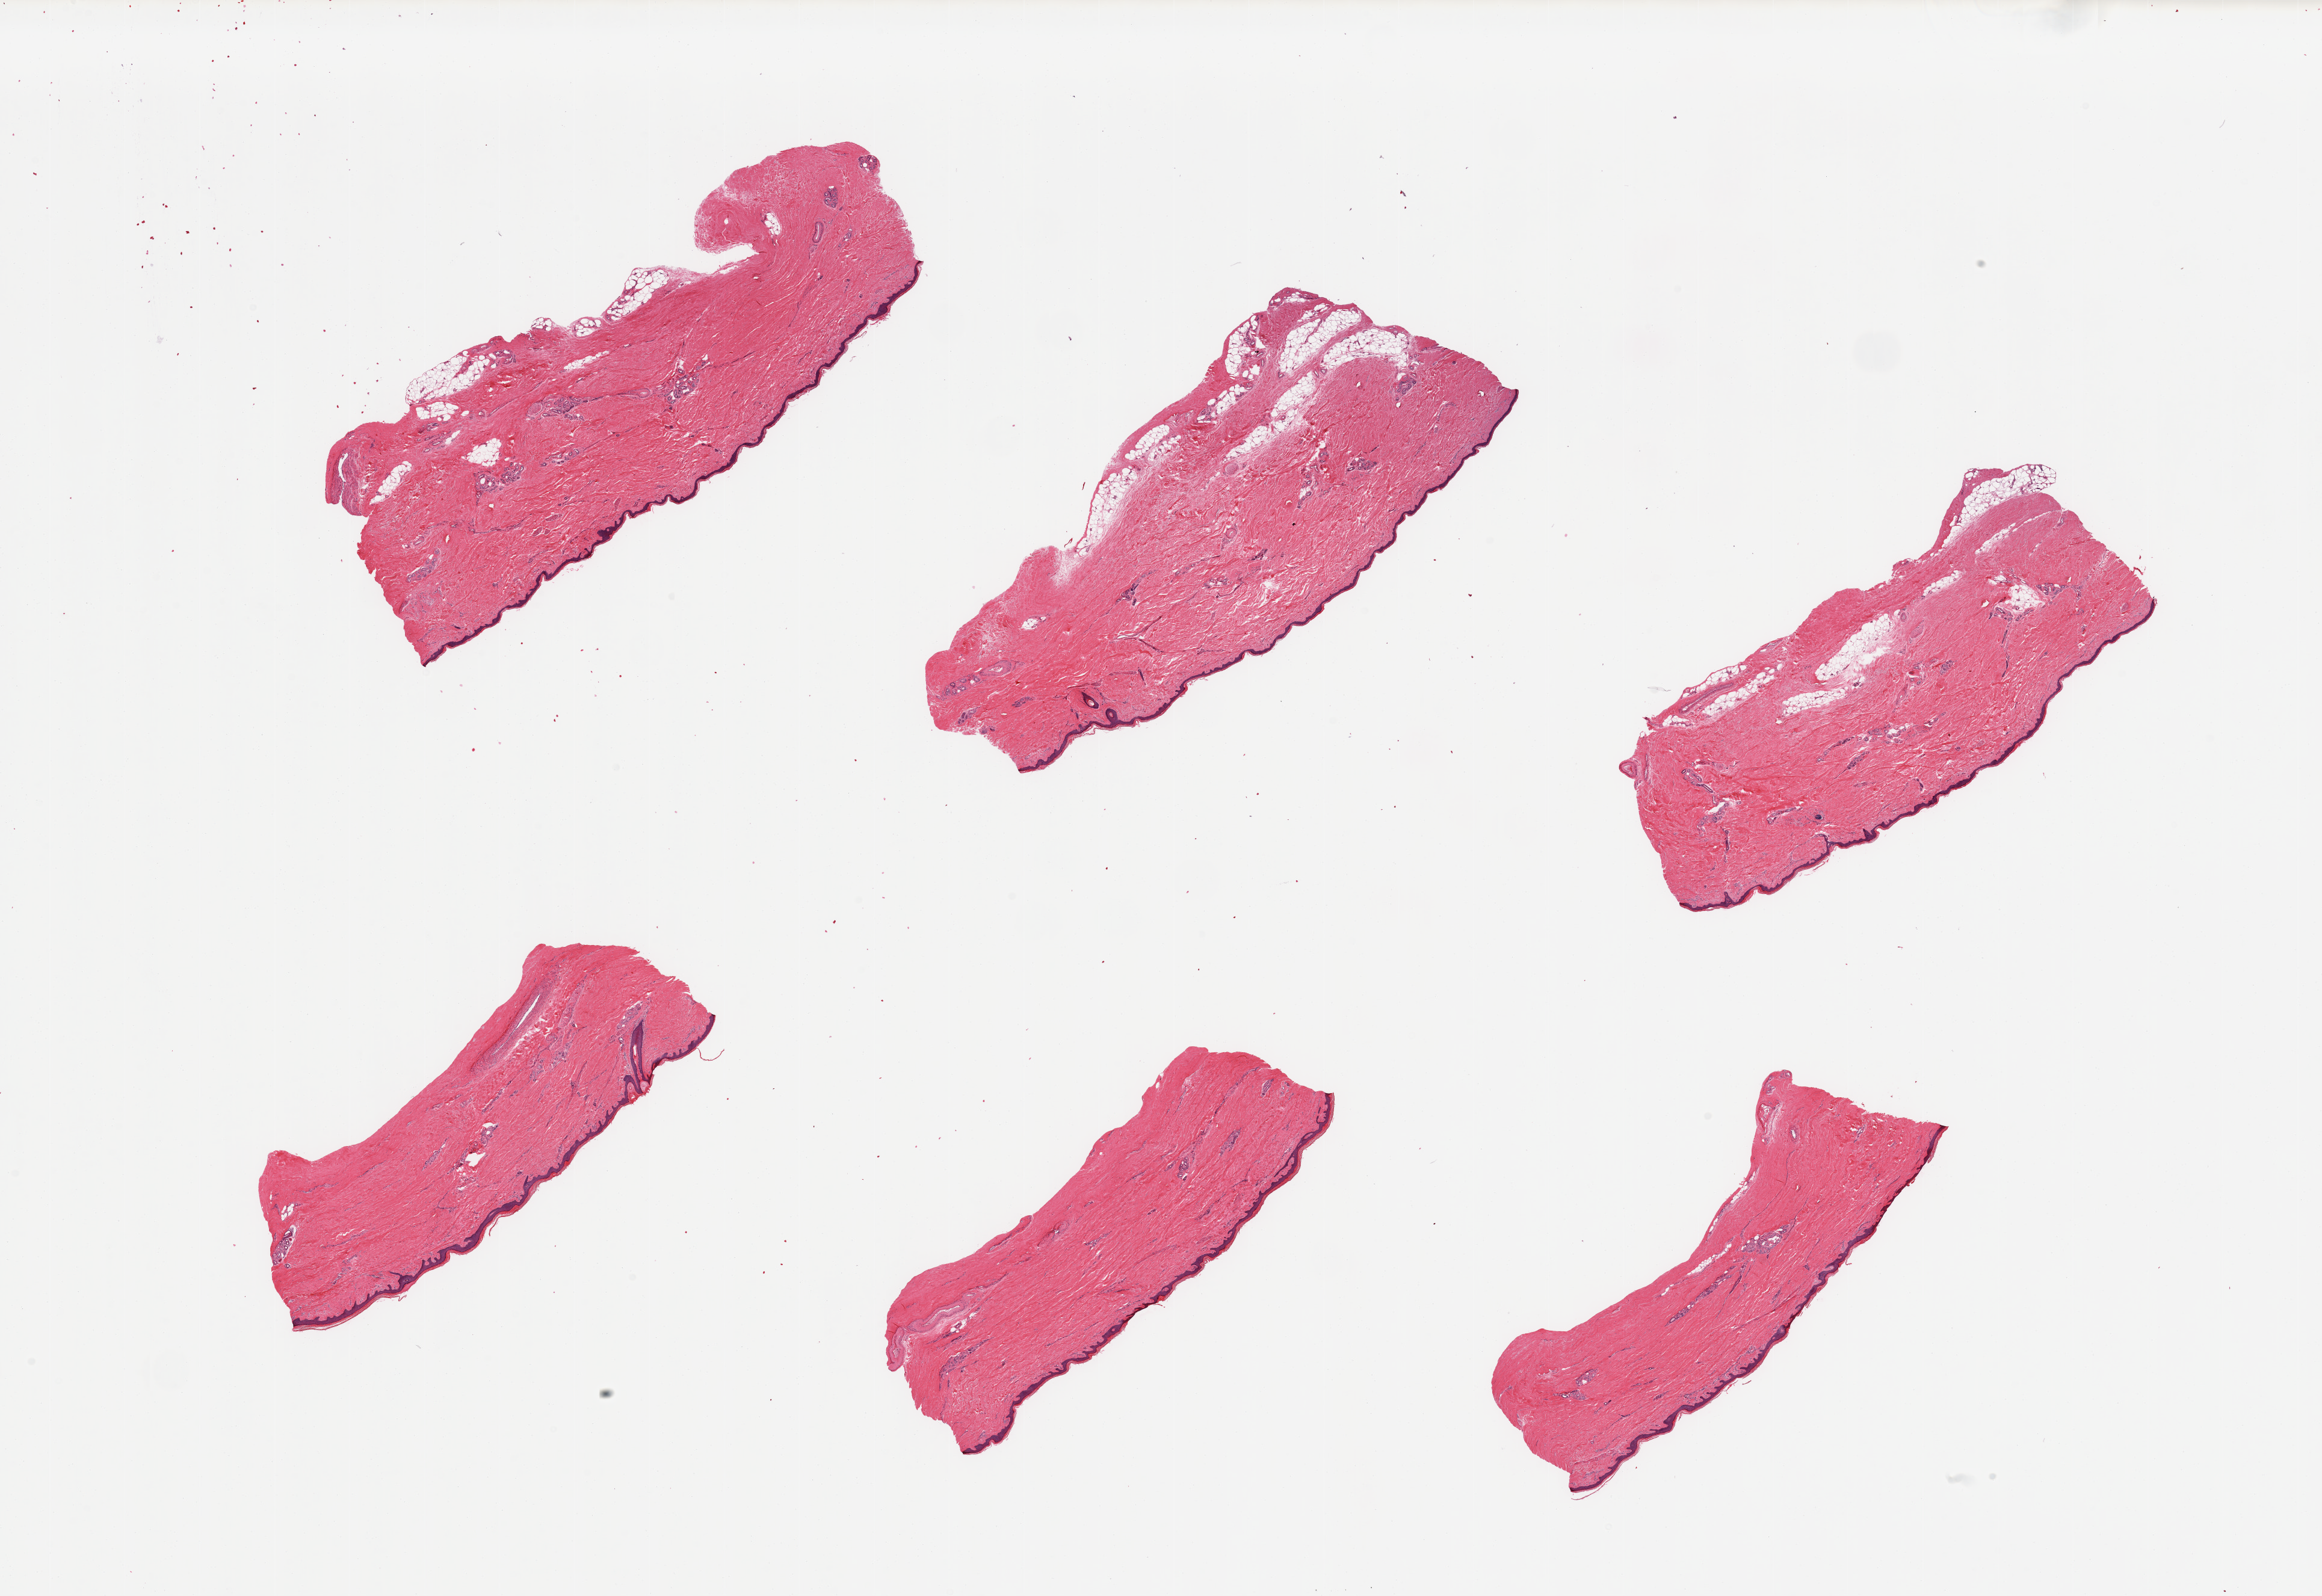
Whole-slide image, haematoxylin and eosin stain — shown as a low-resolution overview of the whole scanned area (about 30.5 x 21.0 mm, acquisition: 20x scan). PAXgene-fixed, paraffin-embedded tissue. Section of skin of lower leg (target tissue). Donor tissue sample. Donor sex: male.
Reviewer comment on this tissue sample: 6 pieces; mostly well trimmed, few with up to ~10% primarily internal fat, epidermis measures 35 microns.